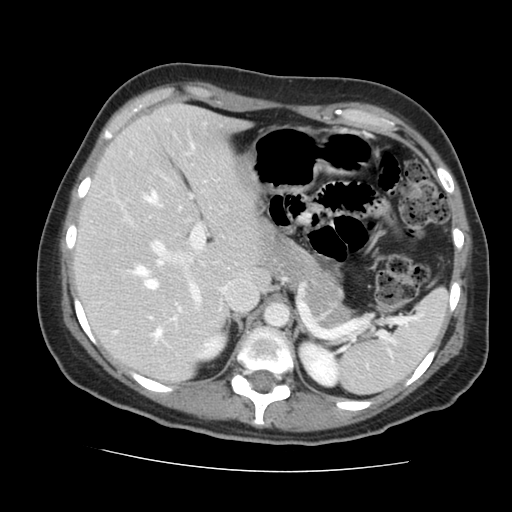
Contrast-enhanced abdominal CT, one axial slice; soft-tissue window (W 400 / L 40 HU); 2.5 mm slice thickness; 512 × 512 image matrix. Female patient, age 46 years. From the clinical record (not read from this slice): diagnosis: colorectal cancer liver metastases, imaged before liver resection; multiple liver metastases: no; largest metastasis: 2.8 cm; disease in both lobes: no.
Annotated regions visible in this slice (outlined manually by an expert reader):
- hepatic veins: bounding box <145,193,162,289> (left, top, right, bottom; pixels)
- liver: <78,106,269,380>
- planned liver remnant (the part of the liver to remain after resection): <78,106,269,380>
- portal vein (with intrahepatic branches): <114,196,205,340>